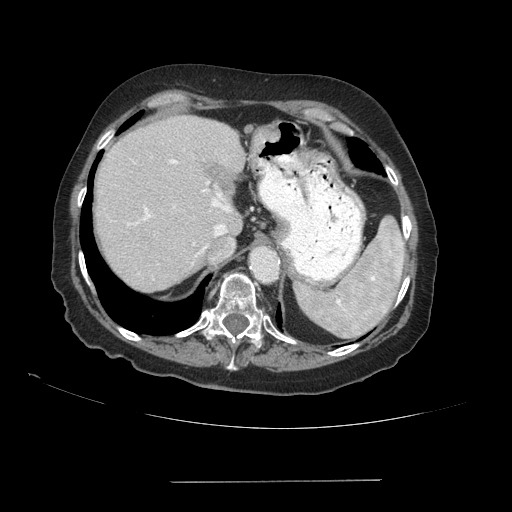
Contrast-enhanced abdominal CT (liver protocol), one axial slice. Slice 68 of 89 in the series (ordered by position). 140 kVp. Soft-tissue window (W 400 / L 40 HU). 2.5 mm slice thickness. 512 × 512 image matrix, field of view 400 × 400 mm. From the clinical record (not read from this slice): diagnosis: hepatocellular carcinoma (patient treated with transarterial chemoembolisation; whether this scan precedes or follows treatment is not stated here); TNM stage (as recorded): Stage-IVA; Child-Pugh class: A; tumour differentiation: poorly differentiated; tumour nodularity: uninodular.
Structures marked on this image (semi-automatic segmentation, software-assisted and operator-edited):
- abdominal aorta: bounding box <252,248,276,280> (left, top, right, bottom; pixels)
- liver parenchyma outside the tumour (the mass and vessels are separate outlines, so this box may not span the whole liver): <94,116,244,290>
- liver vessels: <128,159,230,255>